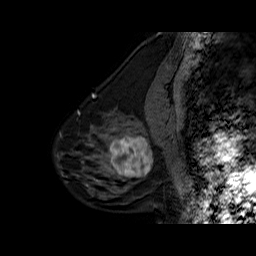
Breast MRI (dynamic contrast-enhanced), one sagittal slice. Slice 20 of 60 in the series (ordered by position). Dynamic contrast-enhanced series, time point 2 of 6 at this slice position (early post-contrast). 1.5 T. TE 6.3 ms, TR 32.5 ms. 4 mm slice thickness. 256 × 256 image matrix, field of view 200 × 200 mm. Female patient. From the clinical record (not read from this slice): setting: breast cancer imaged before/during neoadjuvant chemotherapy; receptor status: triple-negative.
Annotated regions visible in this slice (semi-automatically segmented with operator editing):
- analysis volume of interest (the breast-tissue region the enhancement analysis was run in; not a lesion): bounding box <102,127,162,186> (left, top, right, bottom; pixels)
- tumour enhancement mask (voxels above the 100 % enhancement threshold inside the analysis volume of interest): <109,137,153,177>